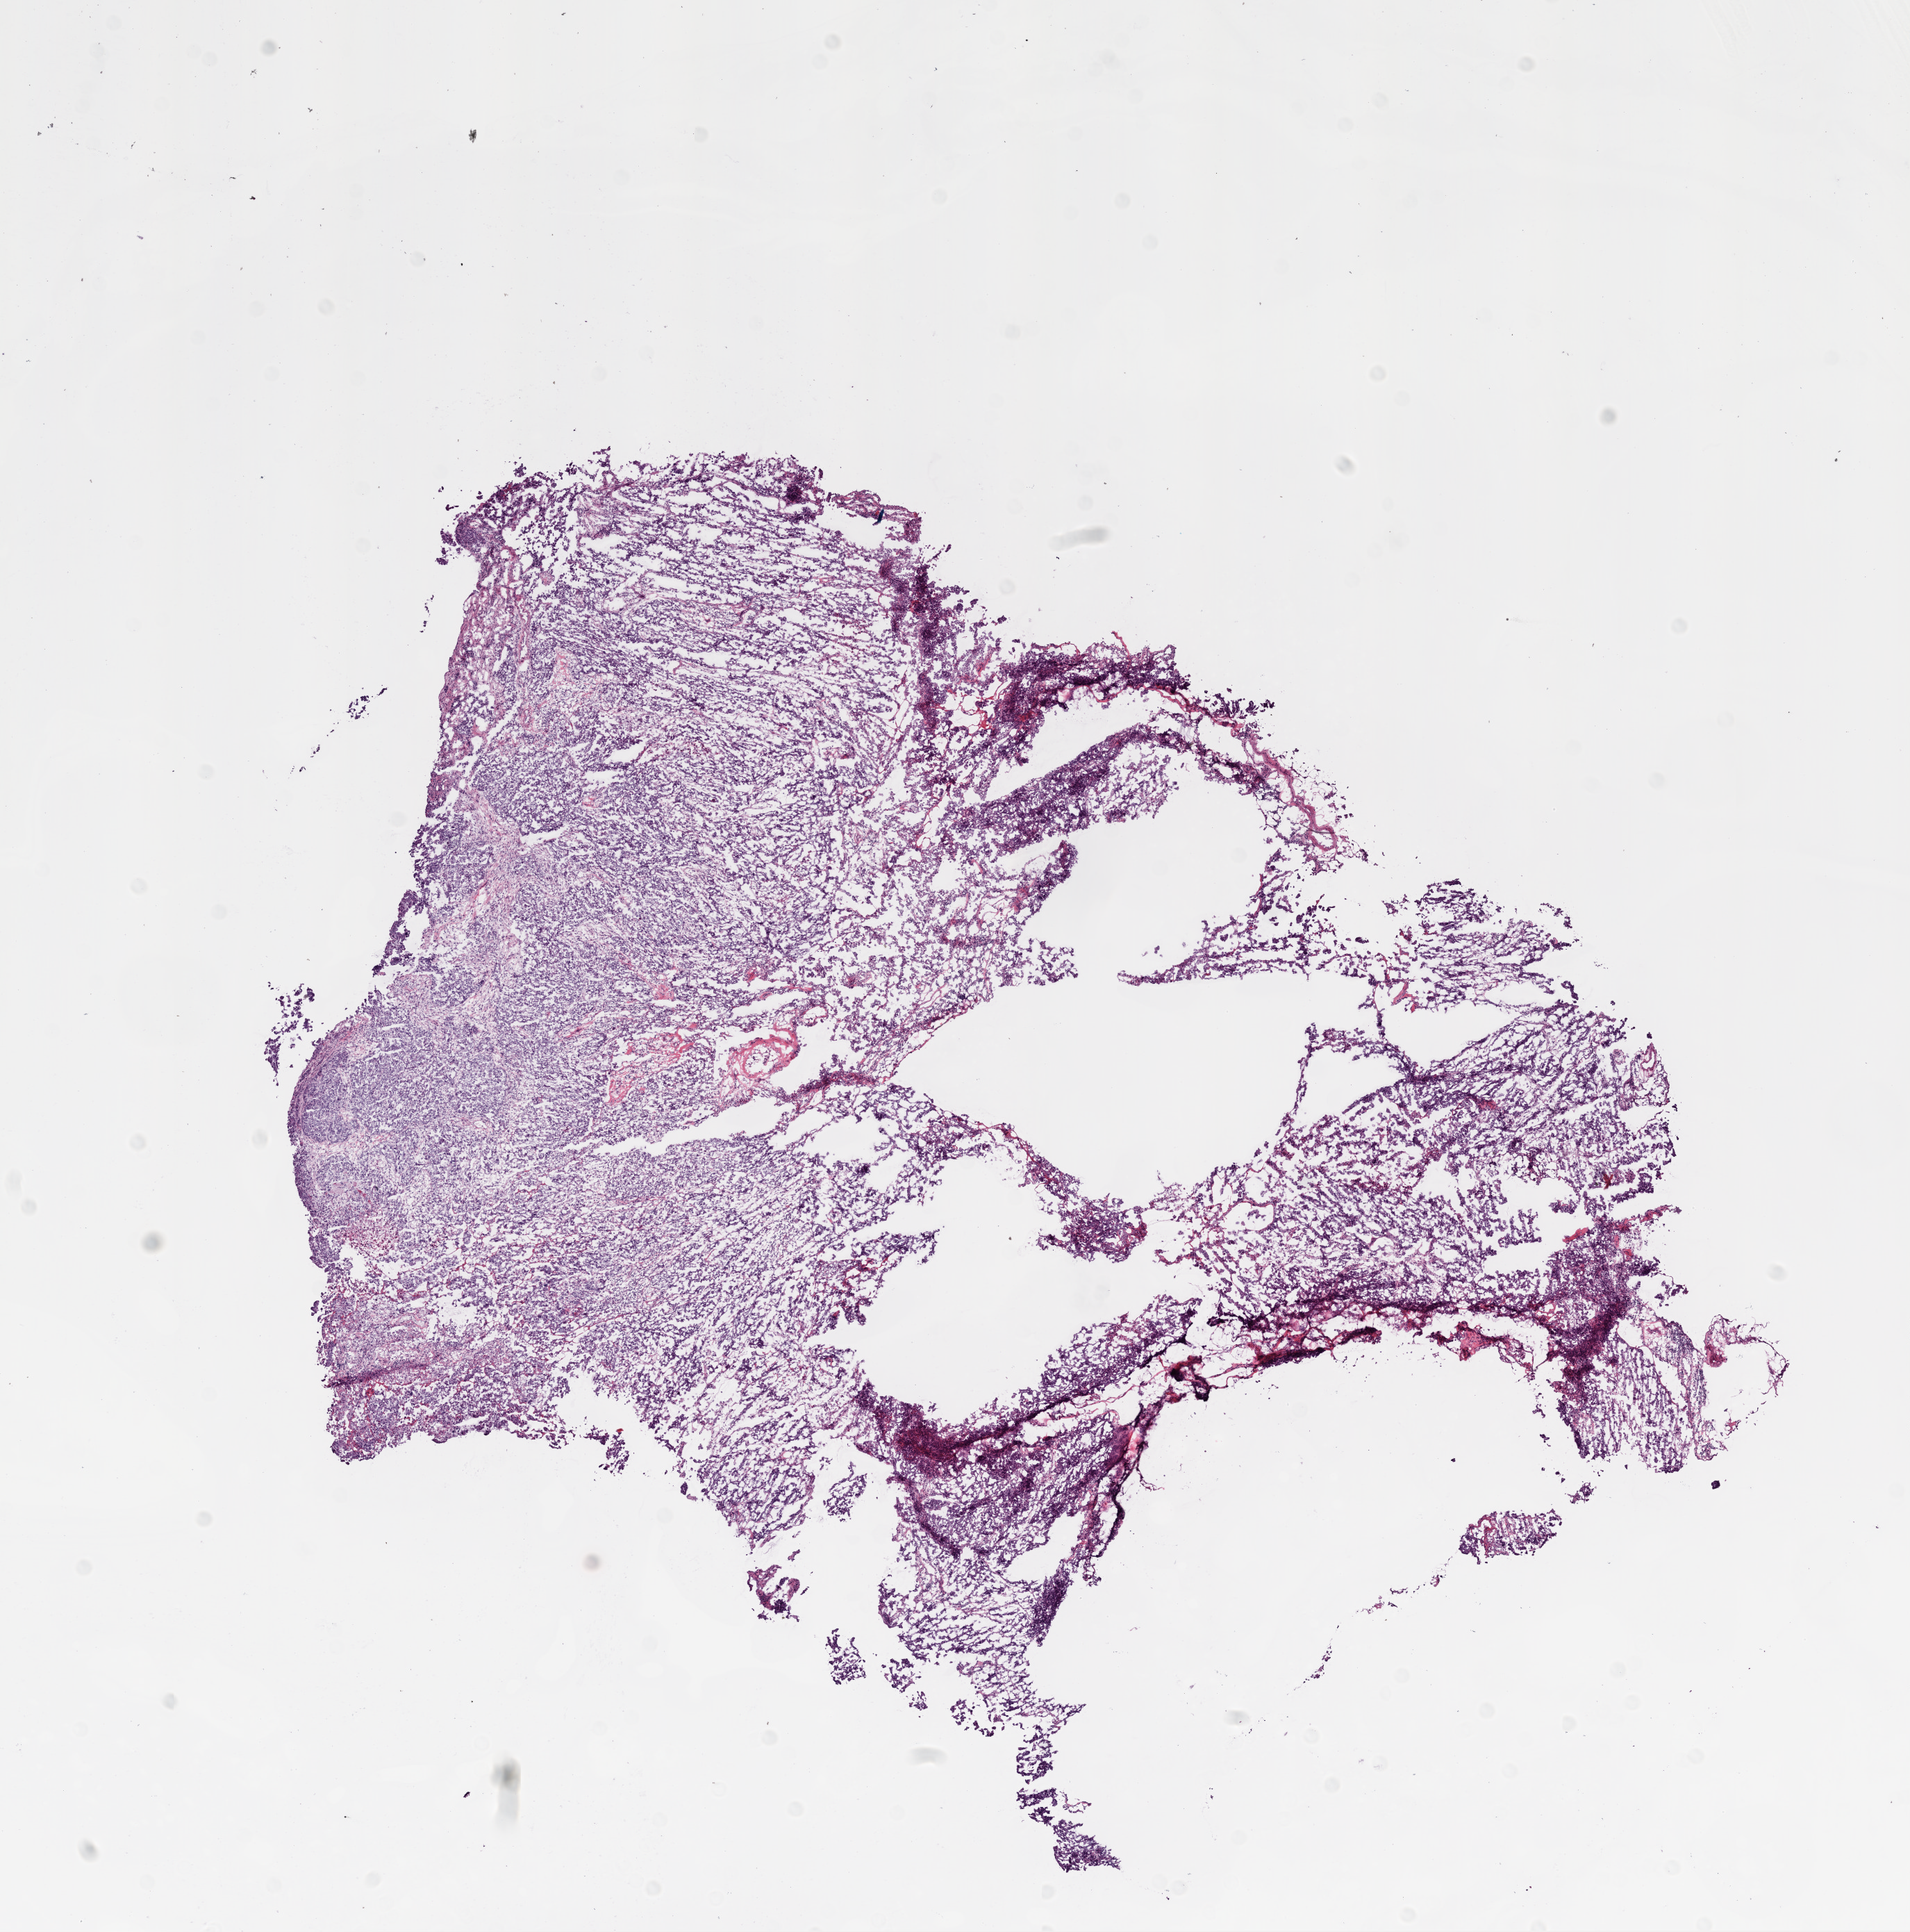
Hematoxylin and eosin (H&E) stained whole-slide image — shown as a low-resolution overview of the whole scanned area (about 11.0 x 11.2 mm, from a 20x scan); frozen section from the bottom of the tissue portion; primary tumour sample from the ovary. Female patient; age at initial diagnosis 56 years. Histologic grade: G3 (poorly differentiated). Pathologist review of this section (percent, as recorded): tumour cells 95%, tumour nuclei 99%, normal cells 0%, stromal cells 5%, necrosis 0%.
FIGO stage: IIIC. Diagnosis: Serous cystadenocarcinoma, NOS.